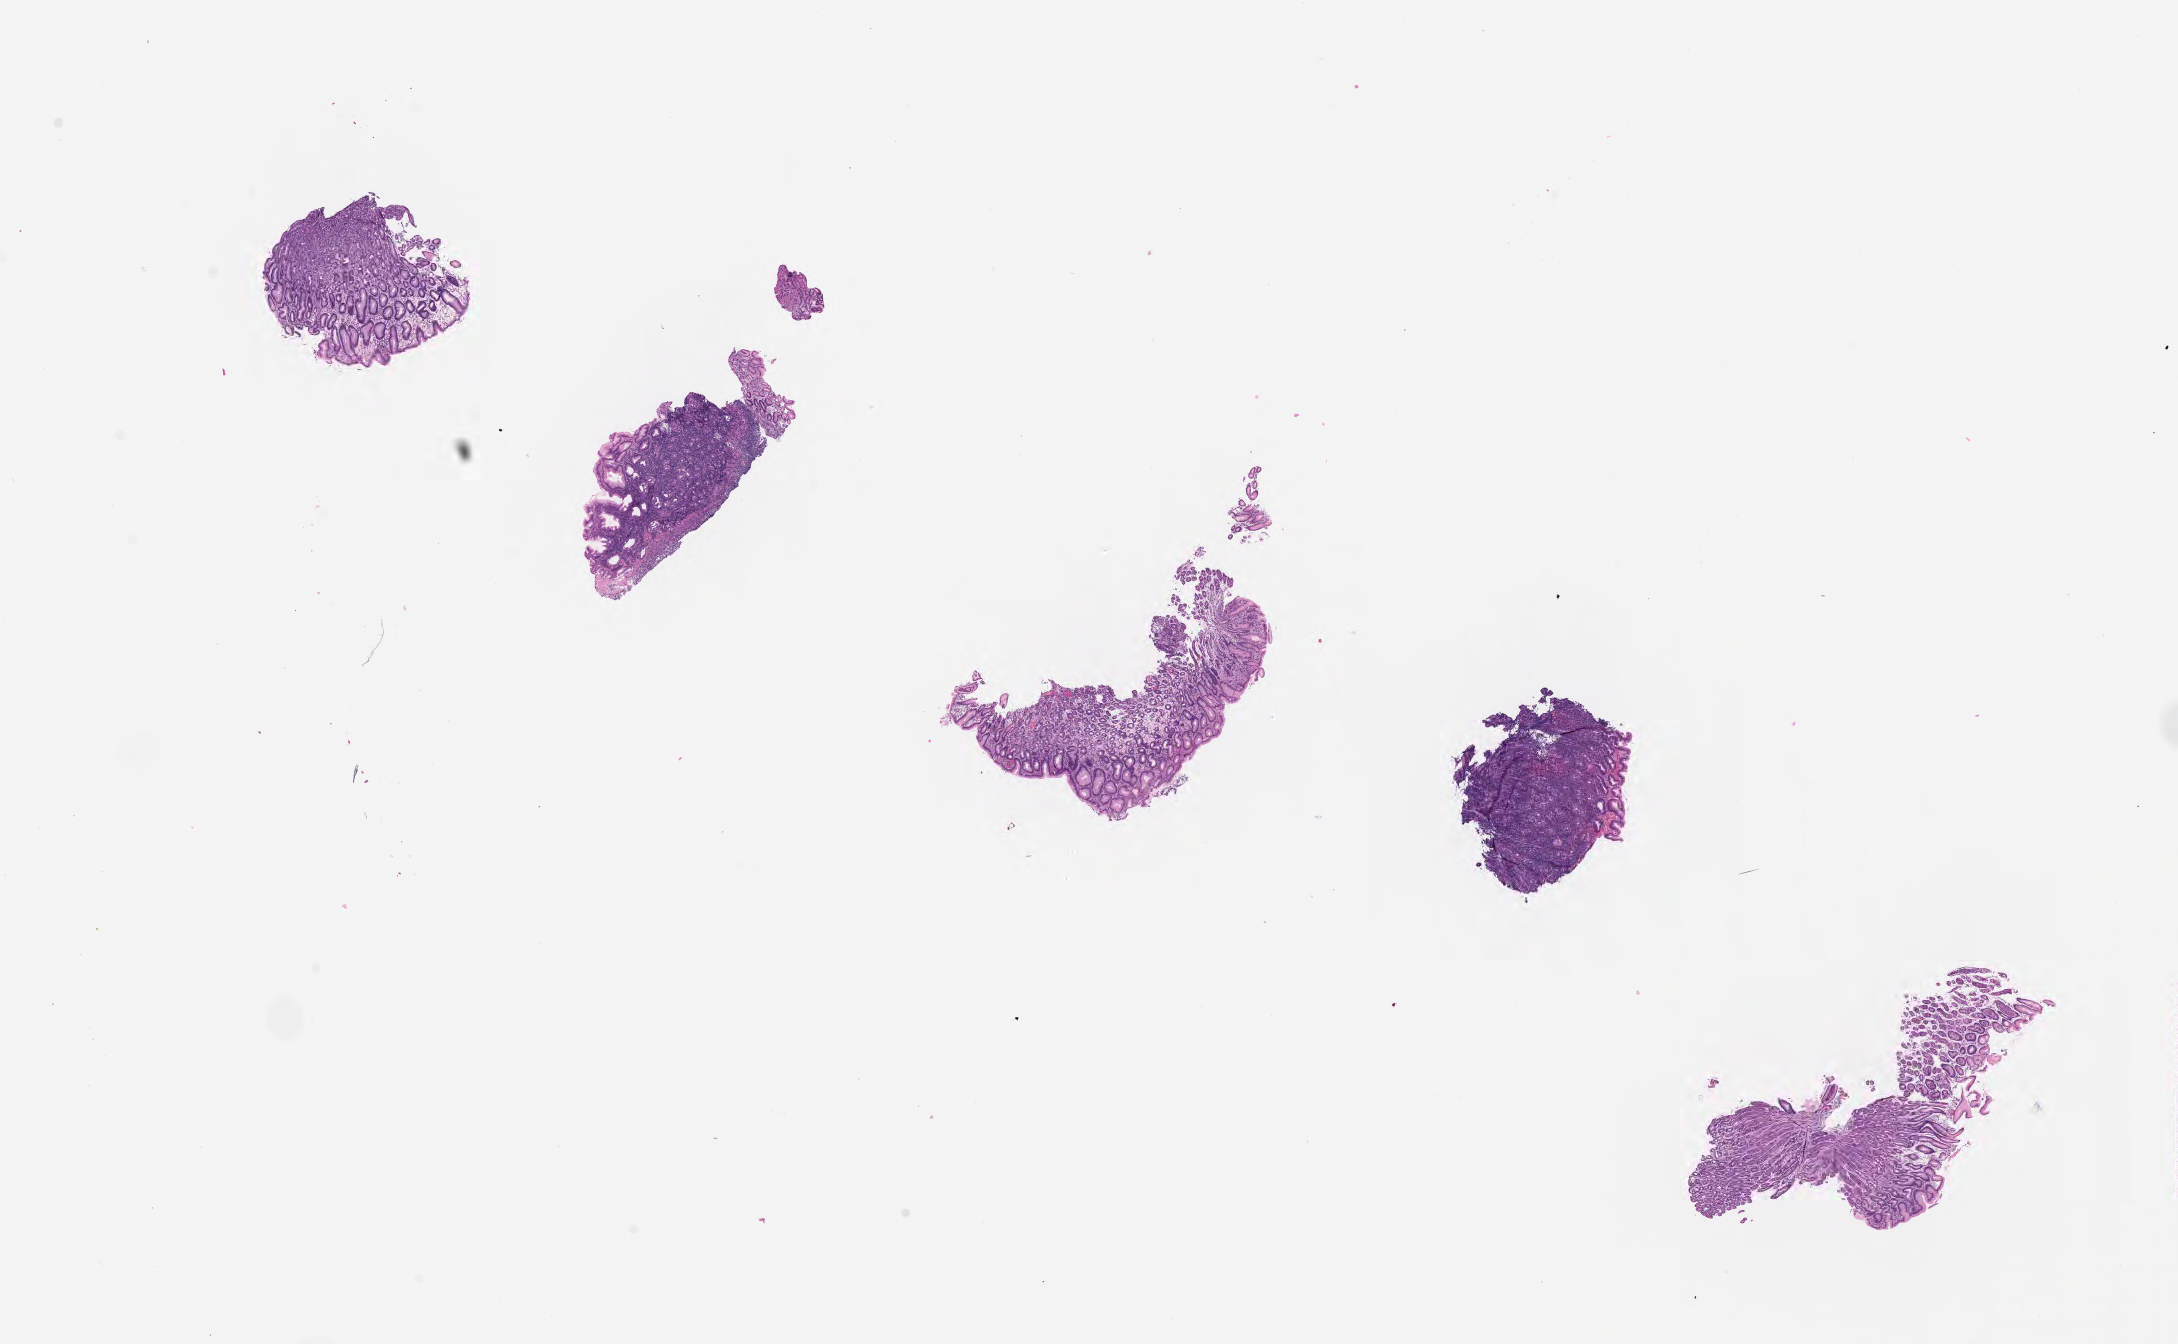
Whole-slide image, H&E stain, a low-resolution overview of the entire scanned area, about 17.6 x 10.9 mm; formalin-fixed, paraffin-embedded (FFPE) tissue; primary tumor. Male patient, 40 years old. Pathologist review of this section (percent, as recorded): tumor cells 40%, tumor nuclei 60%, stromal cells 10%, necrosis 0%, normal cells 50%. Inflammatory infiltration, as recorded: lymphocyte infiltration 50%, monocyte infiltration 20%, neutrophil infiltration 20%.
- Ann Arbor stage (patient): Stage IV
- diagnosis: Burkitt lymphoma, NOS